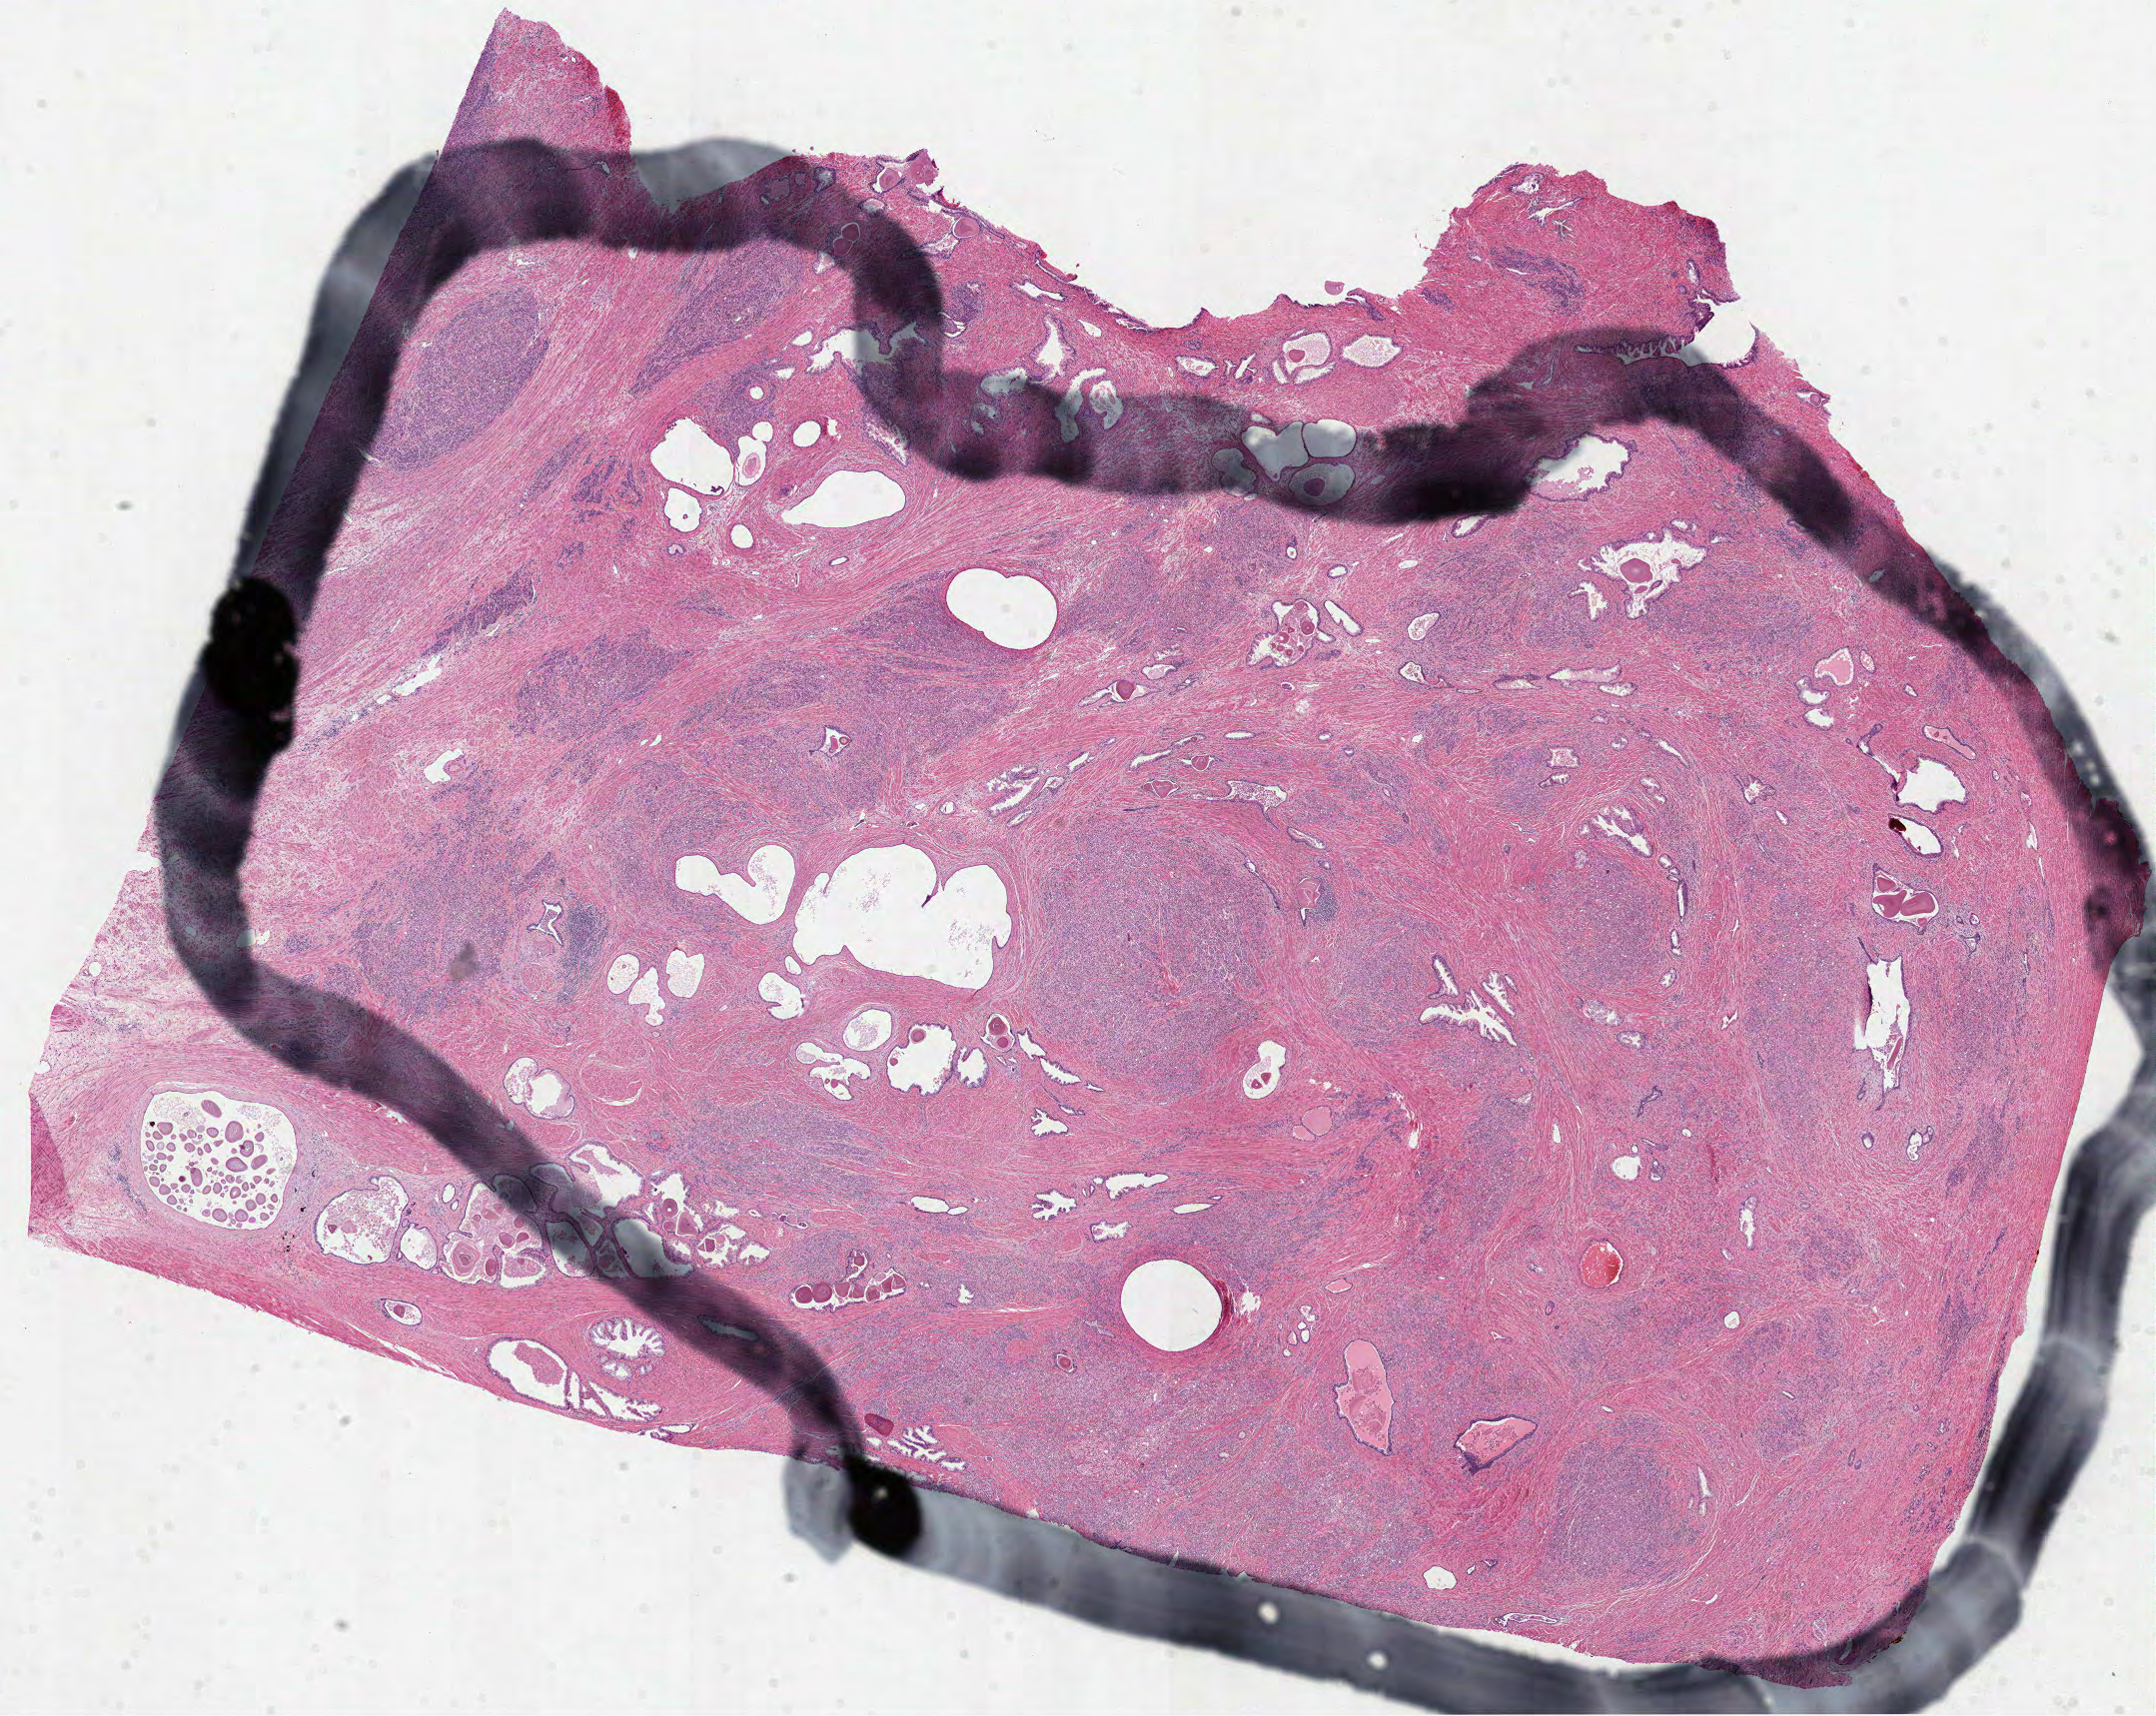
Digitized H&E tissue section (whole slide), low-resolution overview of the scanned area, about 17.4 x 13.9 mm (from a 40x scan); formalin-fixed paraffin-embedded (FFPE) diagnostic section; prostate, primary tumour sample. Male, age 68 years at initial diagnosis. Gleason score: 8 (5+3).
* histologic diagnosis: Acinar cell carcinoma (prostate gland)
* laterality: bilateral